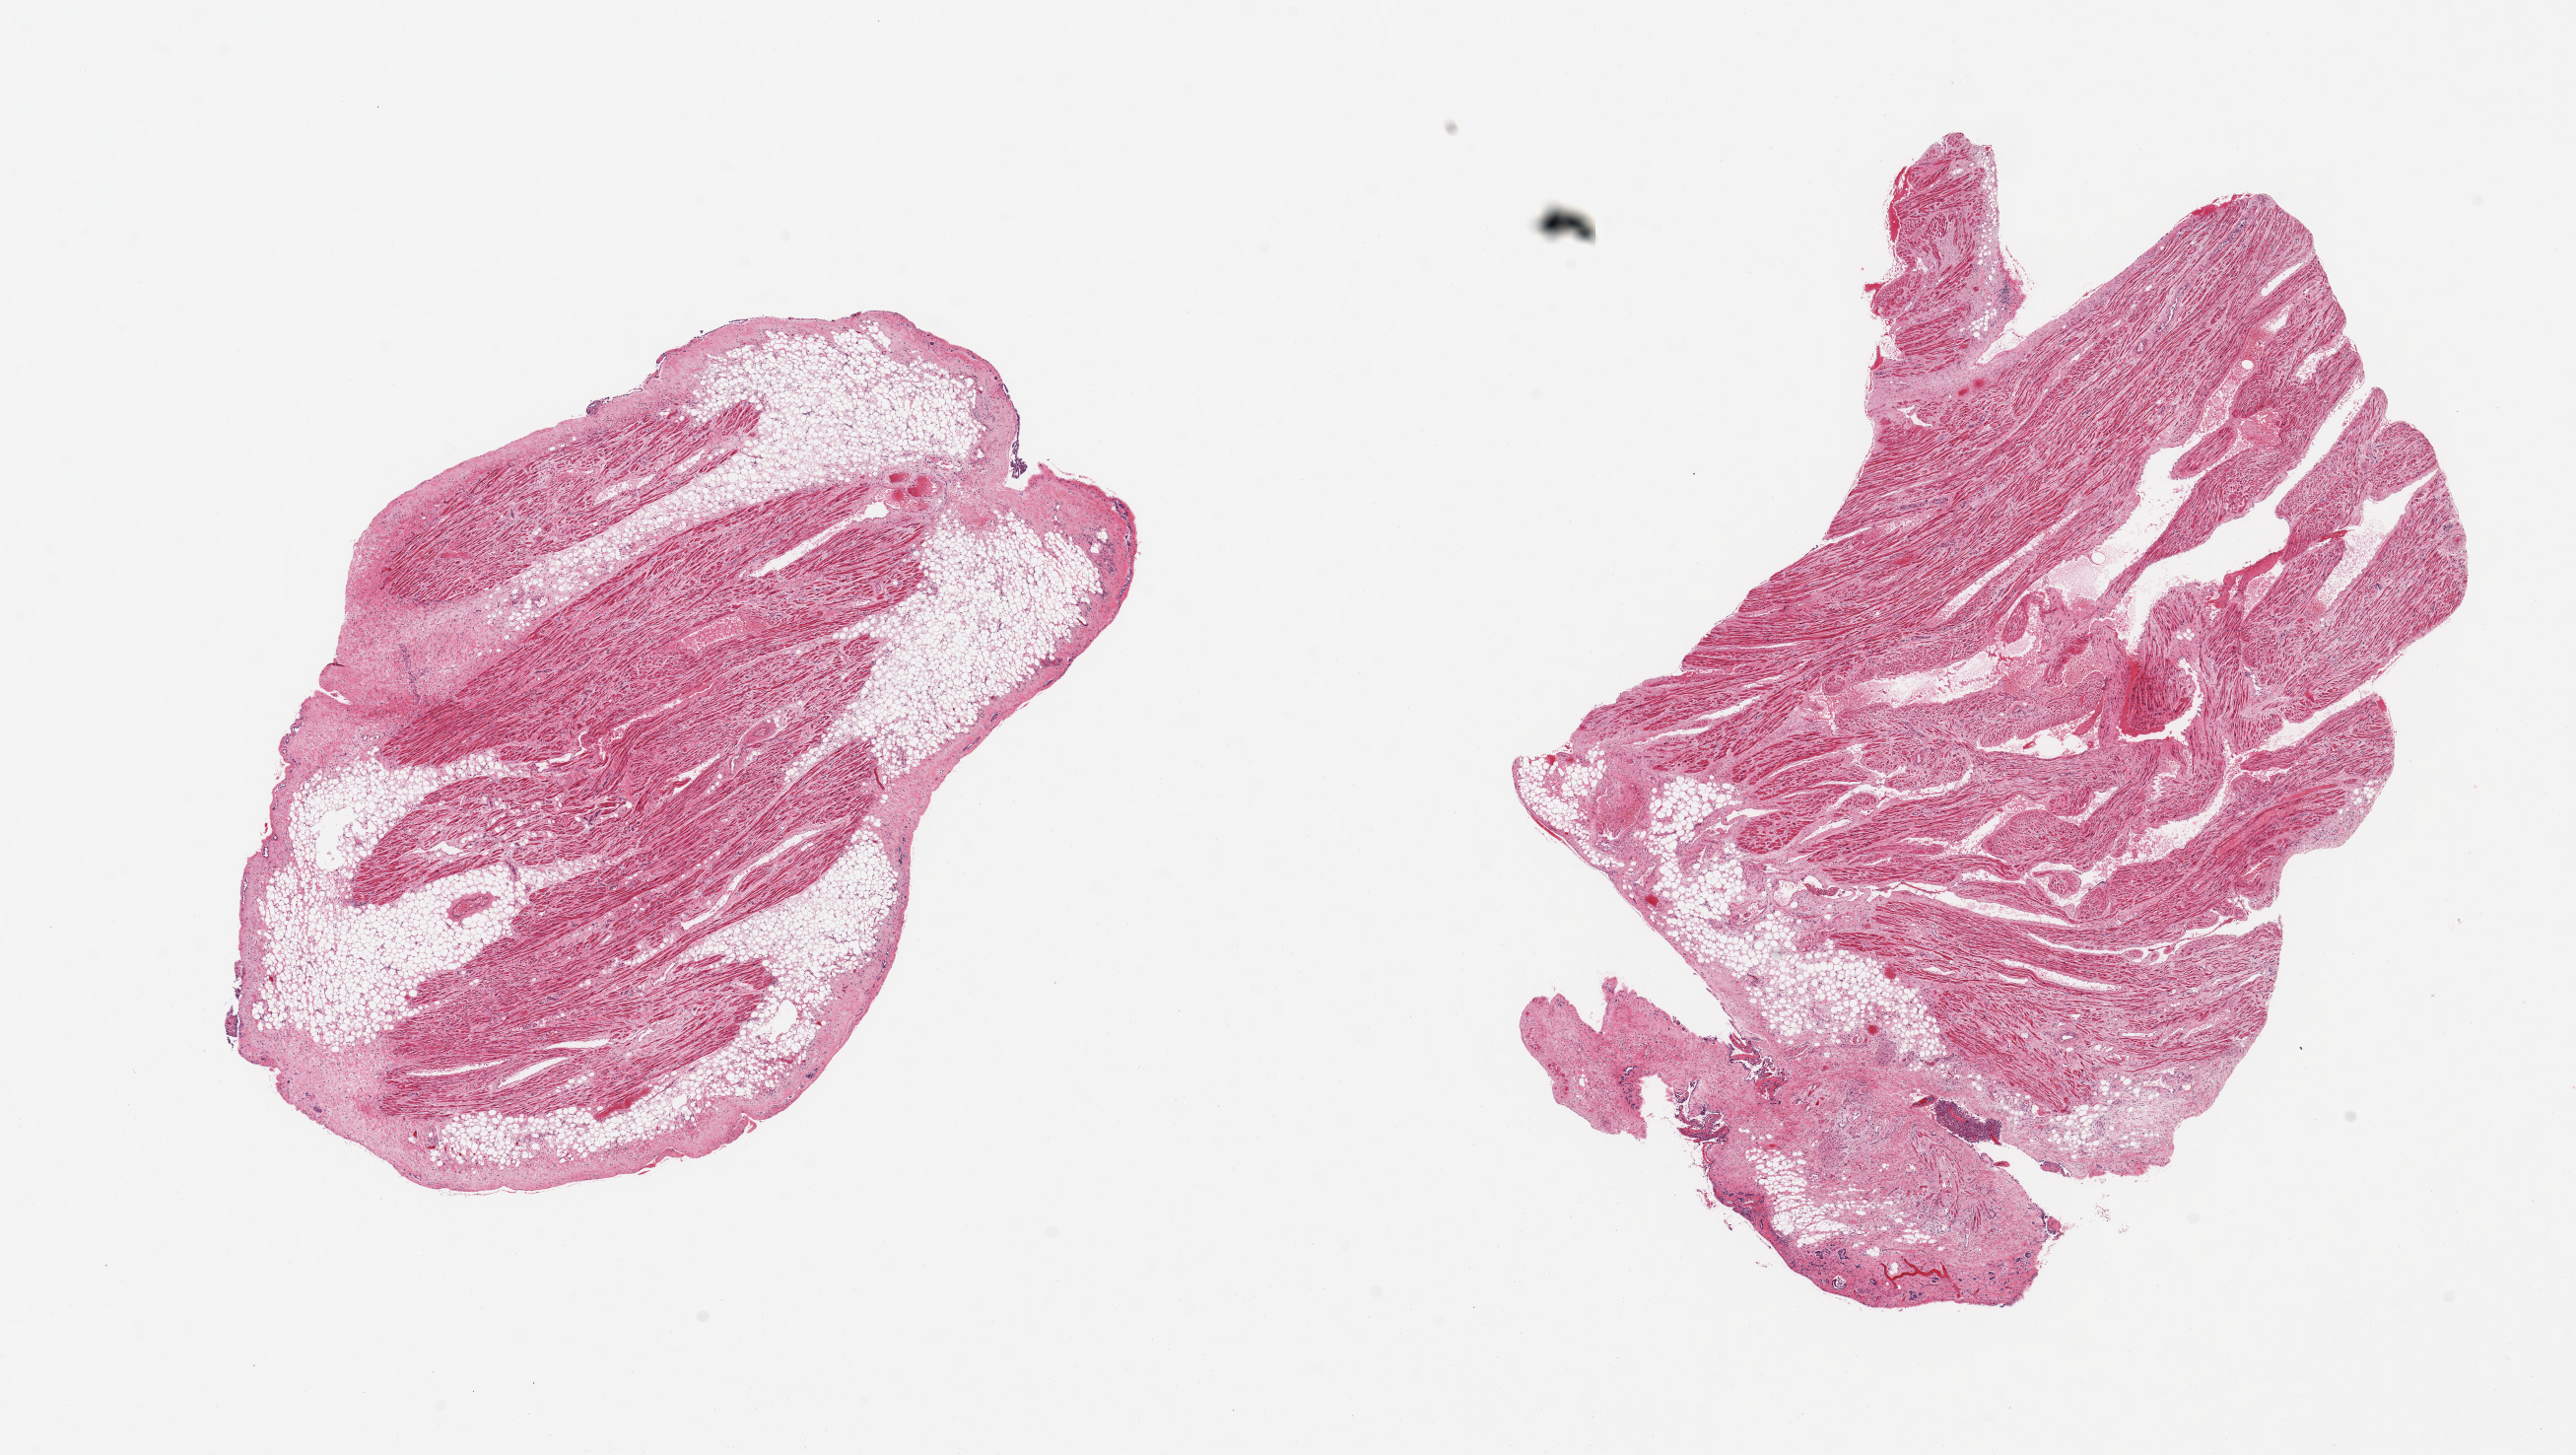
Digitized H&E-stained section — a low-resolution overview of the entire scanned area, about 20.7 x 11.7 mm (slide scanned at 20x); PAXgene-fixed, paraffin-embedded tissue; section of auricular appendage (target tissue); donor tissue sample. Female donor.
Pathologist's review note for this sample: 2 pieces; 50% & 20% fibrofatty content.